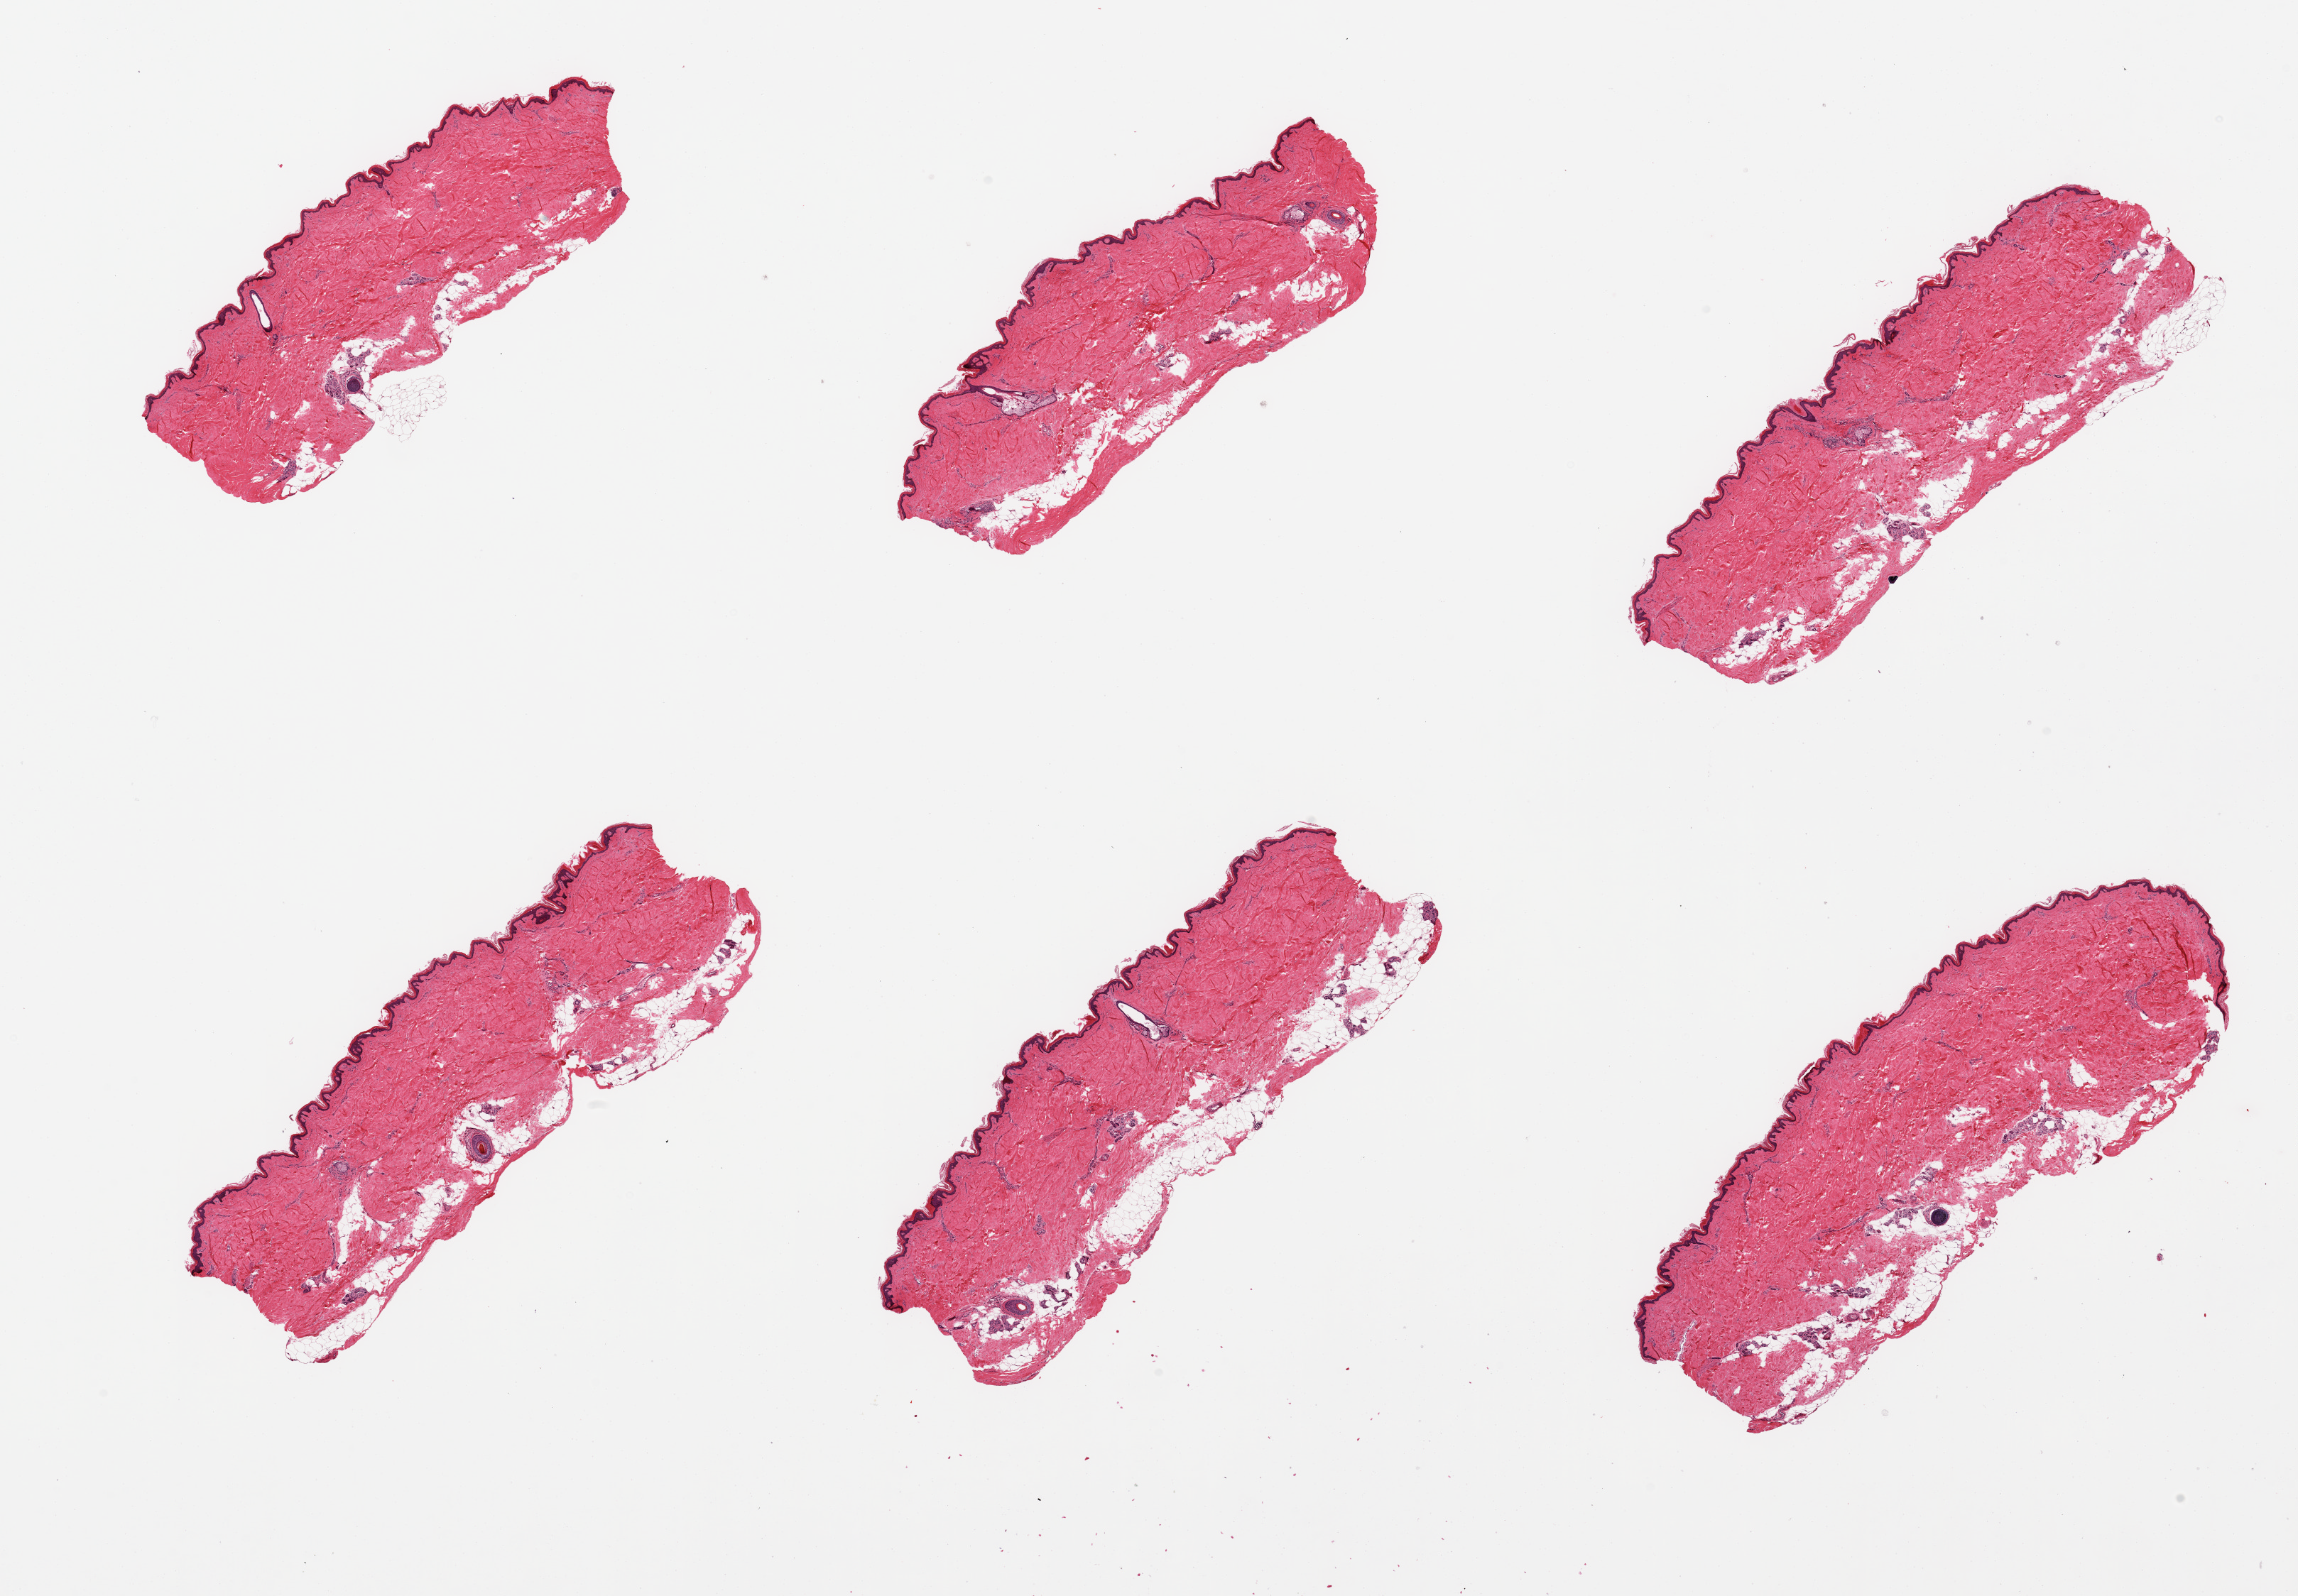
Digitized haematoxylin and eosin-stained section, brightfield, shown as a low-resolution overview of the whole scanned area (about 25.6 x 17.8 mm, acquisition: 20x scan); PAXgene-fixed paraffin-embedded (PFPE) section; target tissue: skin of lower leg; tissue donor sample.
• pathologist's review note for this sample: 6 pieces, trace adherent fat, squamous epithelium is ~40-50 microns